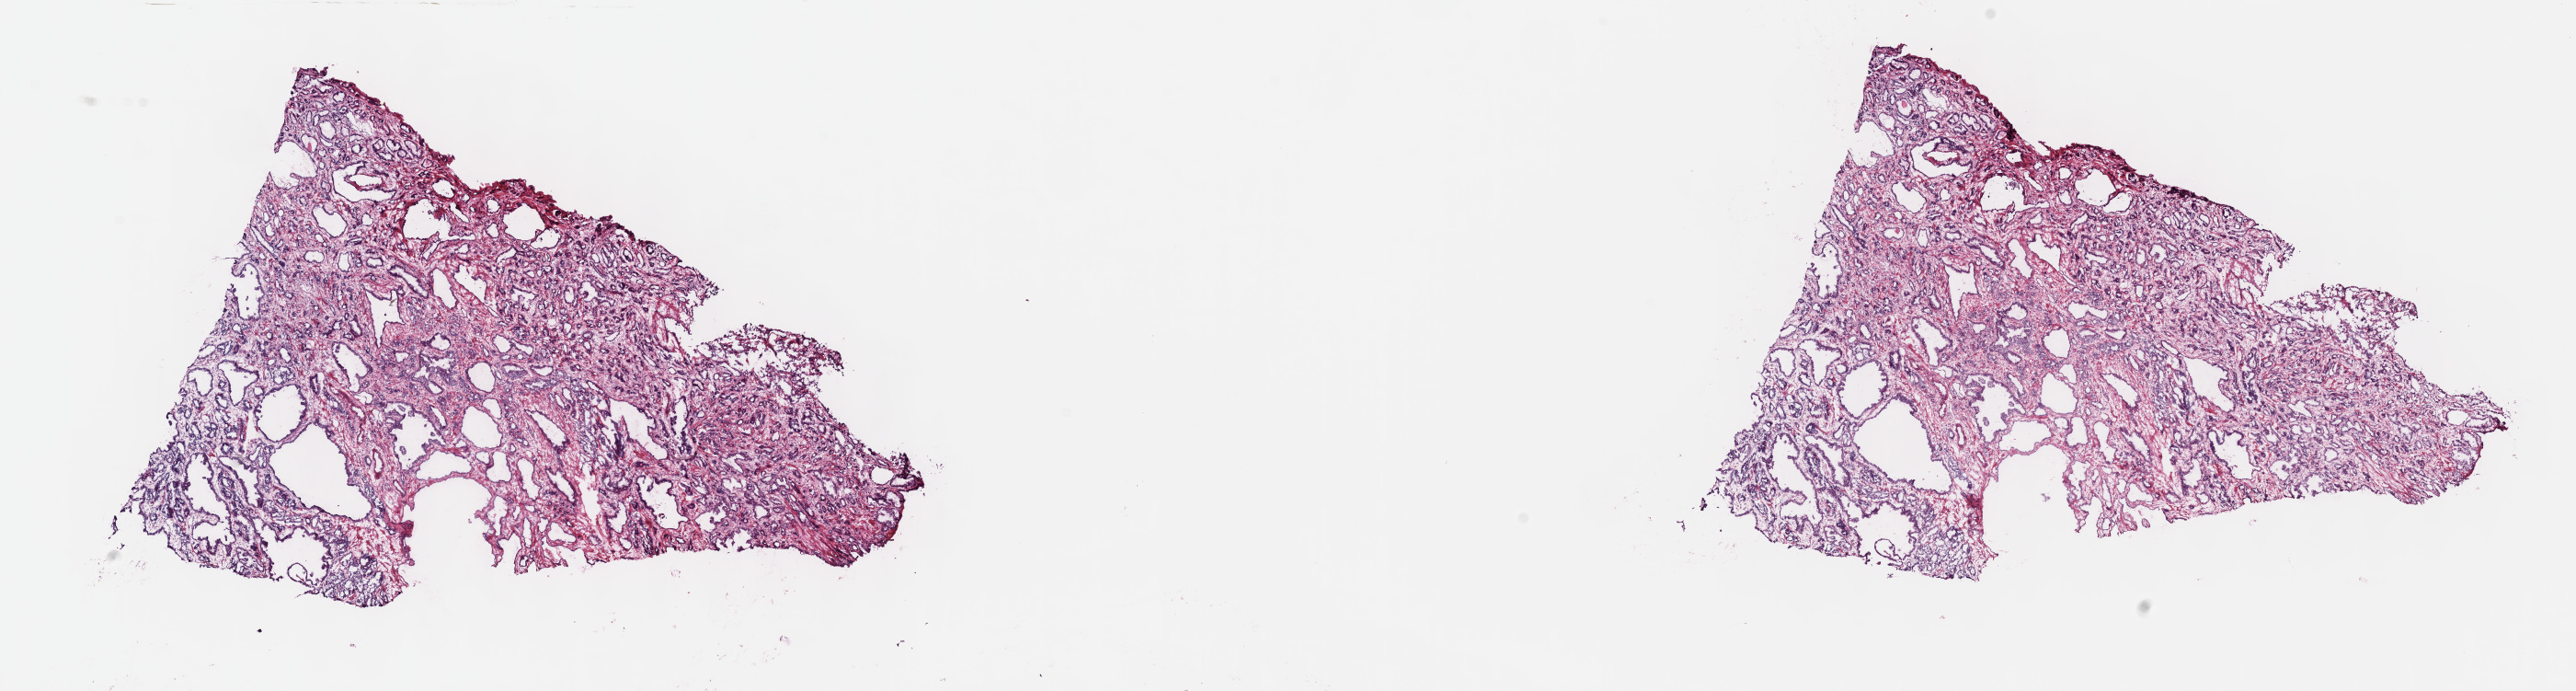
H&E whole-slide image, shown as a low-resolution overview of the whole scanned area (about 22.7 x 6.1 mm, slide scanned at 40x); frozen section from the top of the tissue portion; primary tumour sample from the prostate. Patient: male, age at initial diagnosis 56 years. Gleason score: 7 (3+4). Composition of this section per pathologist review: tumour cells 35%, tumour nuclei 75%, normal cells 20%, stromal cells 45%, necrosis 0%. Infiltration values recorded for this section: lymphocyte infiltration 6%, monocyte infiltration 0%, neutrophil infiltration 0%.
Histologic diagnosis: Adenocarcinoma, NOS (prostate gland).